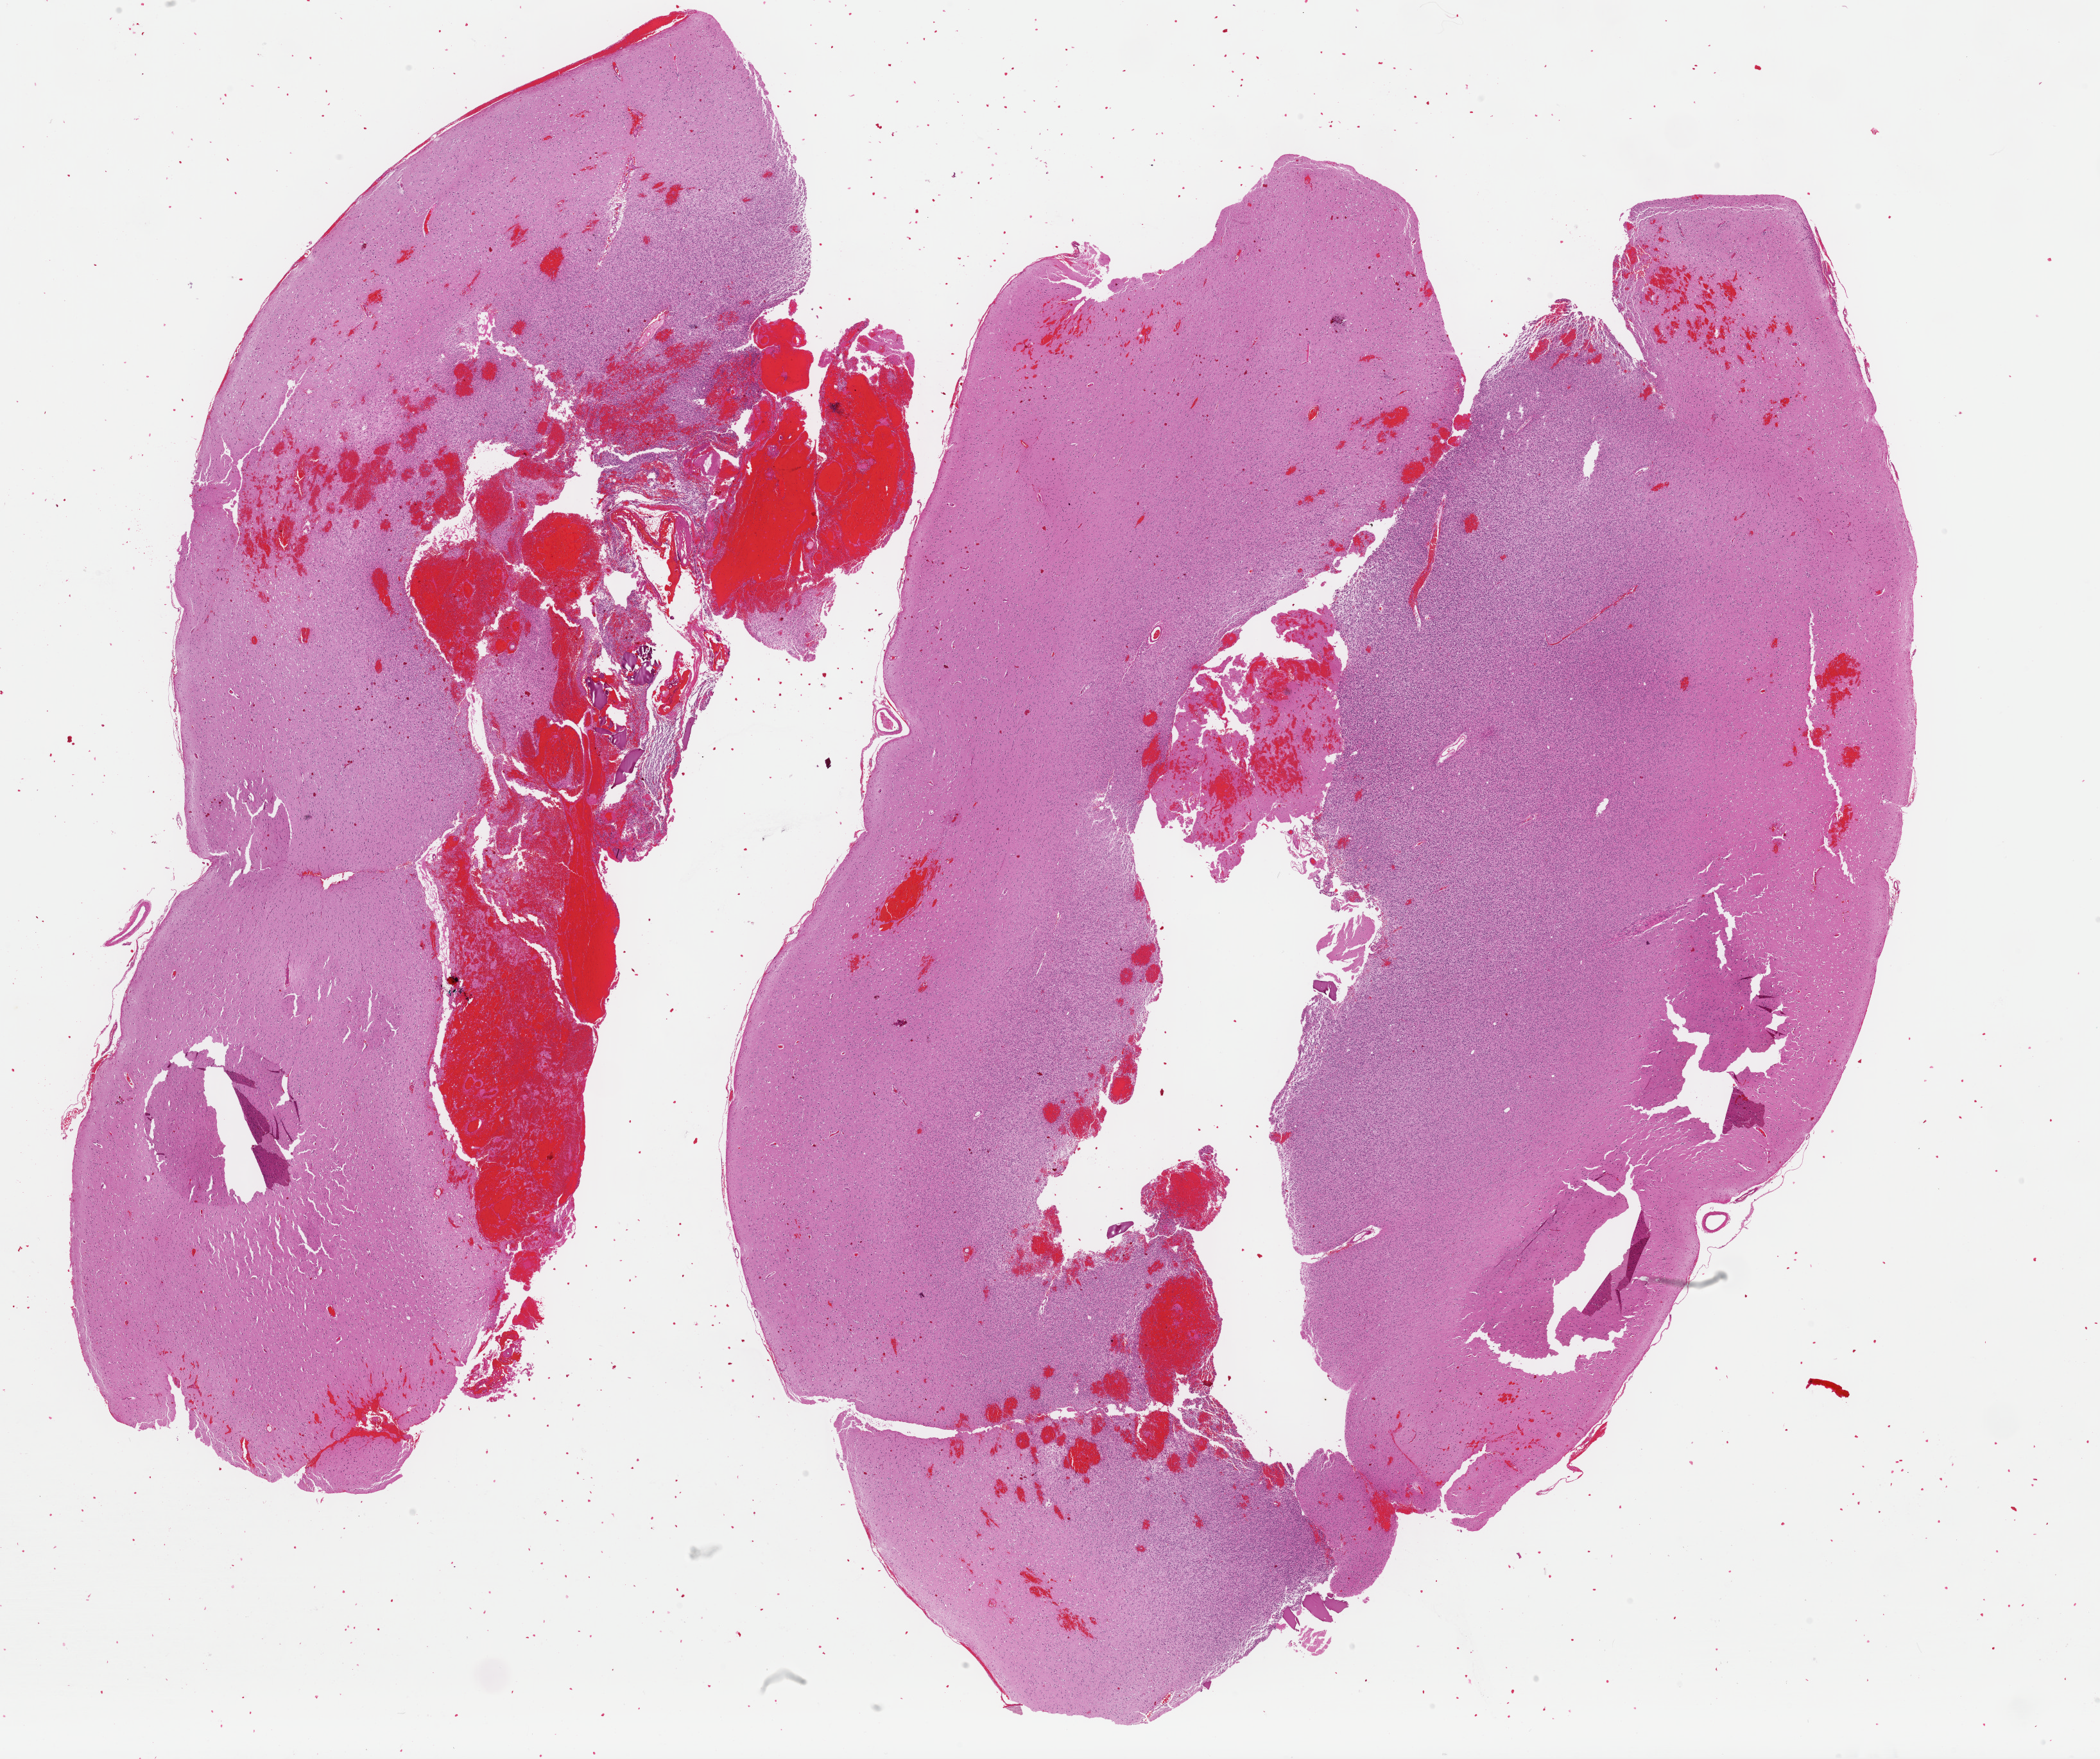
H&E whole-slide image, shown as a low-resolution overview of the whole scanned area (about 25.8 x 21.6 mm, slide scanned at 40x), formalin-fixed paraffin-embedded (FFPE) diagnostic section, recurrent tumour sample from the brain. Female patient; age at initial diagnosis 27 years.
This section: recurrent tumour. Patient diagnosis: Oligodendroglioma, NOS (temporal lobe).